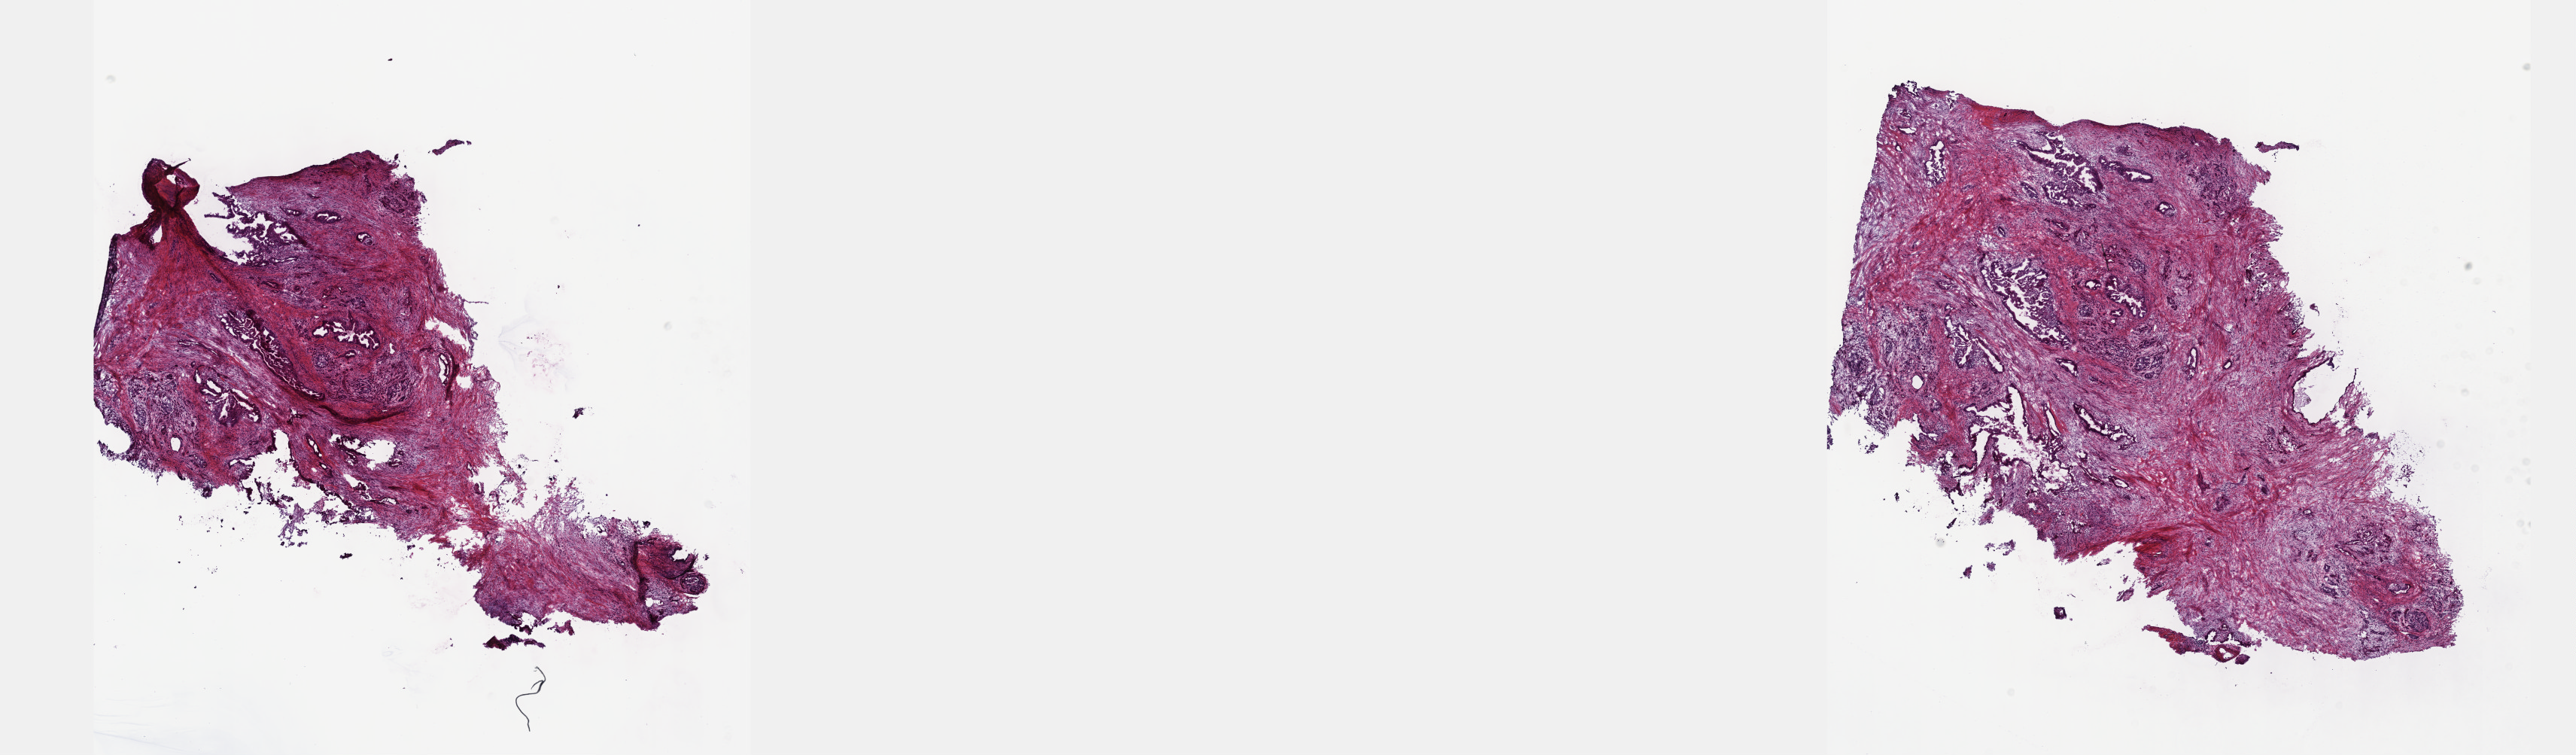
Digitized Hematoxylin and eosin (H&E) stained tissue section (whole slide), a low-resolution overview of the entire scanned area, about 27.7 x 8.1 mm (acquisition: 40x scan). Frozen section from the top of the tissue portion. Sample: primary tumour, pancreas. Male patient; age at initial diagnosis 35 years.
Diagnosis: Infiltrating duct carcinoma, NOS.